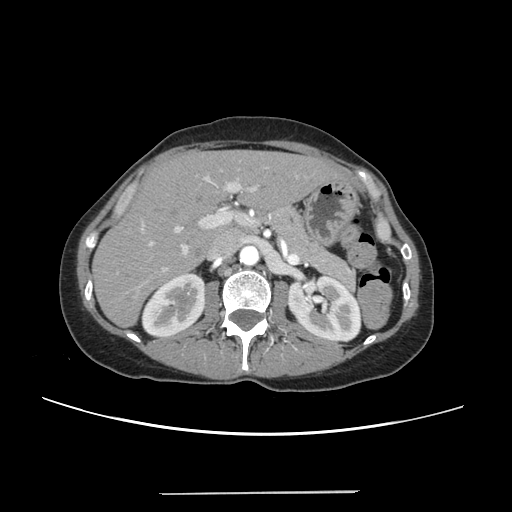
Contrast-enhanced abdominal CT, one axial slice. Position 140 of 240 along the scan axis. 120 kVp. Intravenous contrast given. Soft-tissue window (W 400 / L 40 HU). 512 × 512 image matrix, field of view 371 × 371 mm. Female patient, age 60 years. From the clinical record (not read from this slice): diagnosis: colorectal cancer liver metastases, imaged before liver resection; multiple liver metastases: no; largest metastasis: 1.5 cm; chemotherapy before resection: yes.
Annotated regions visible in this slice (outlined manually by an expert reader):
- liver: box from (x=94, y=151) to (x=343, y=325) px
- planned liver remnant (the part of the liver to remain after resection): (x=94, y=152)–(x=343, y=325)
- portal vein (with intrahepatic branches): (x=140, y=171)–(x=298, y=271)